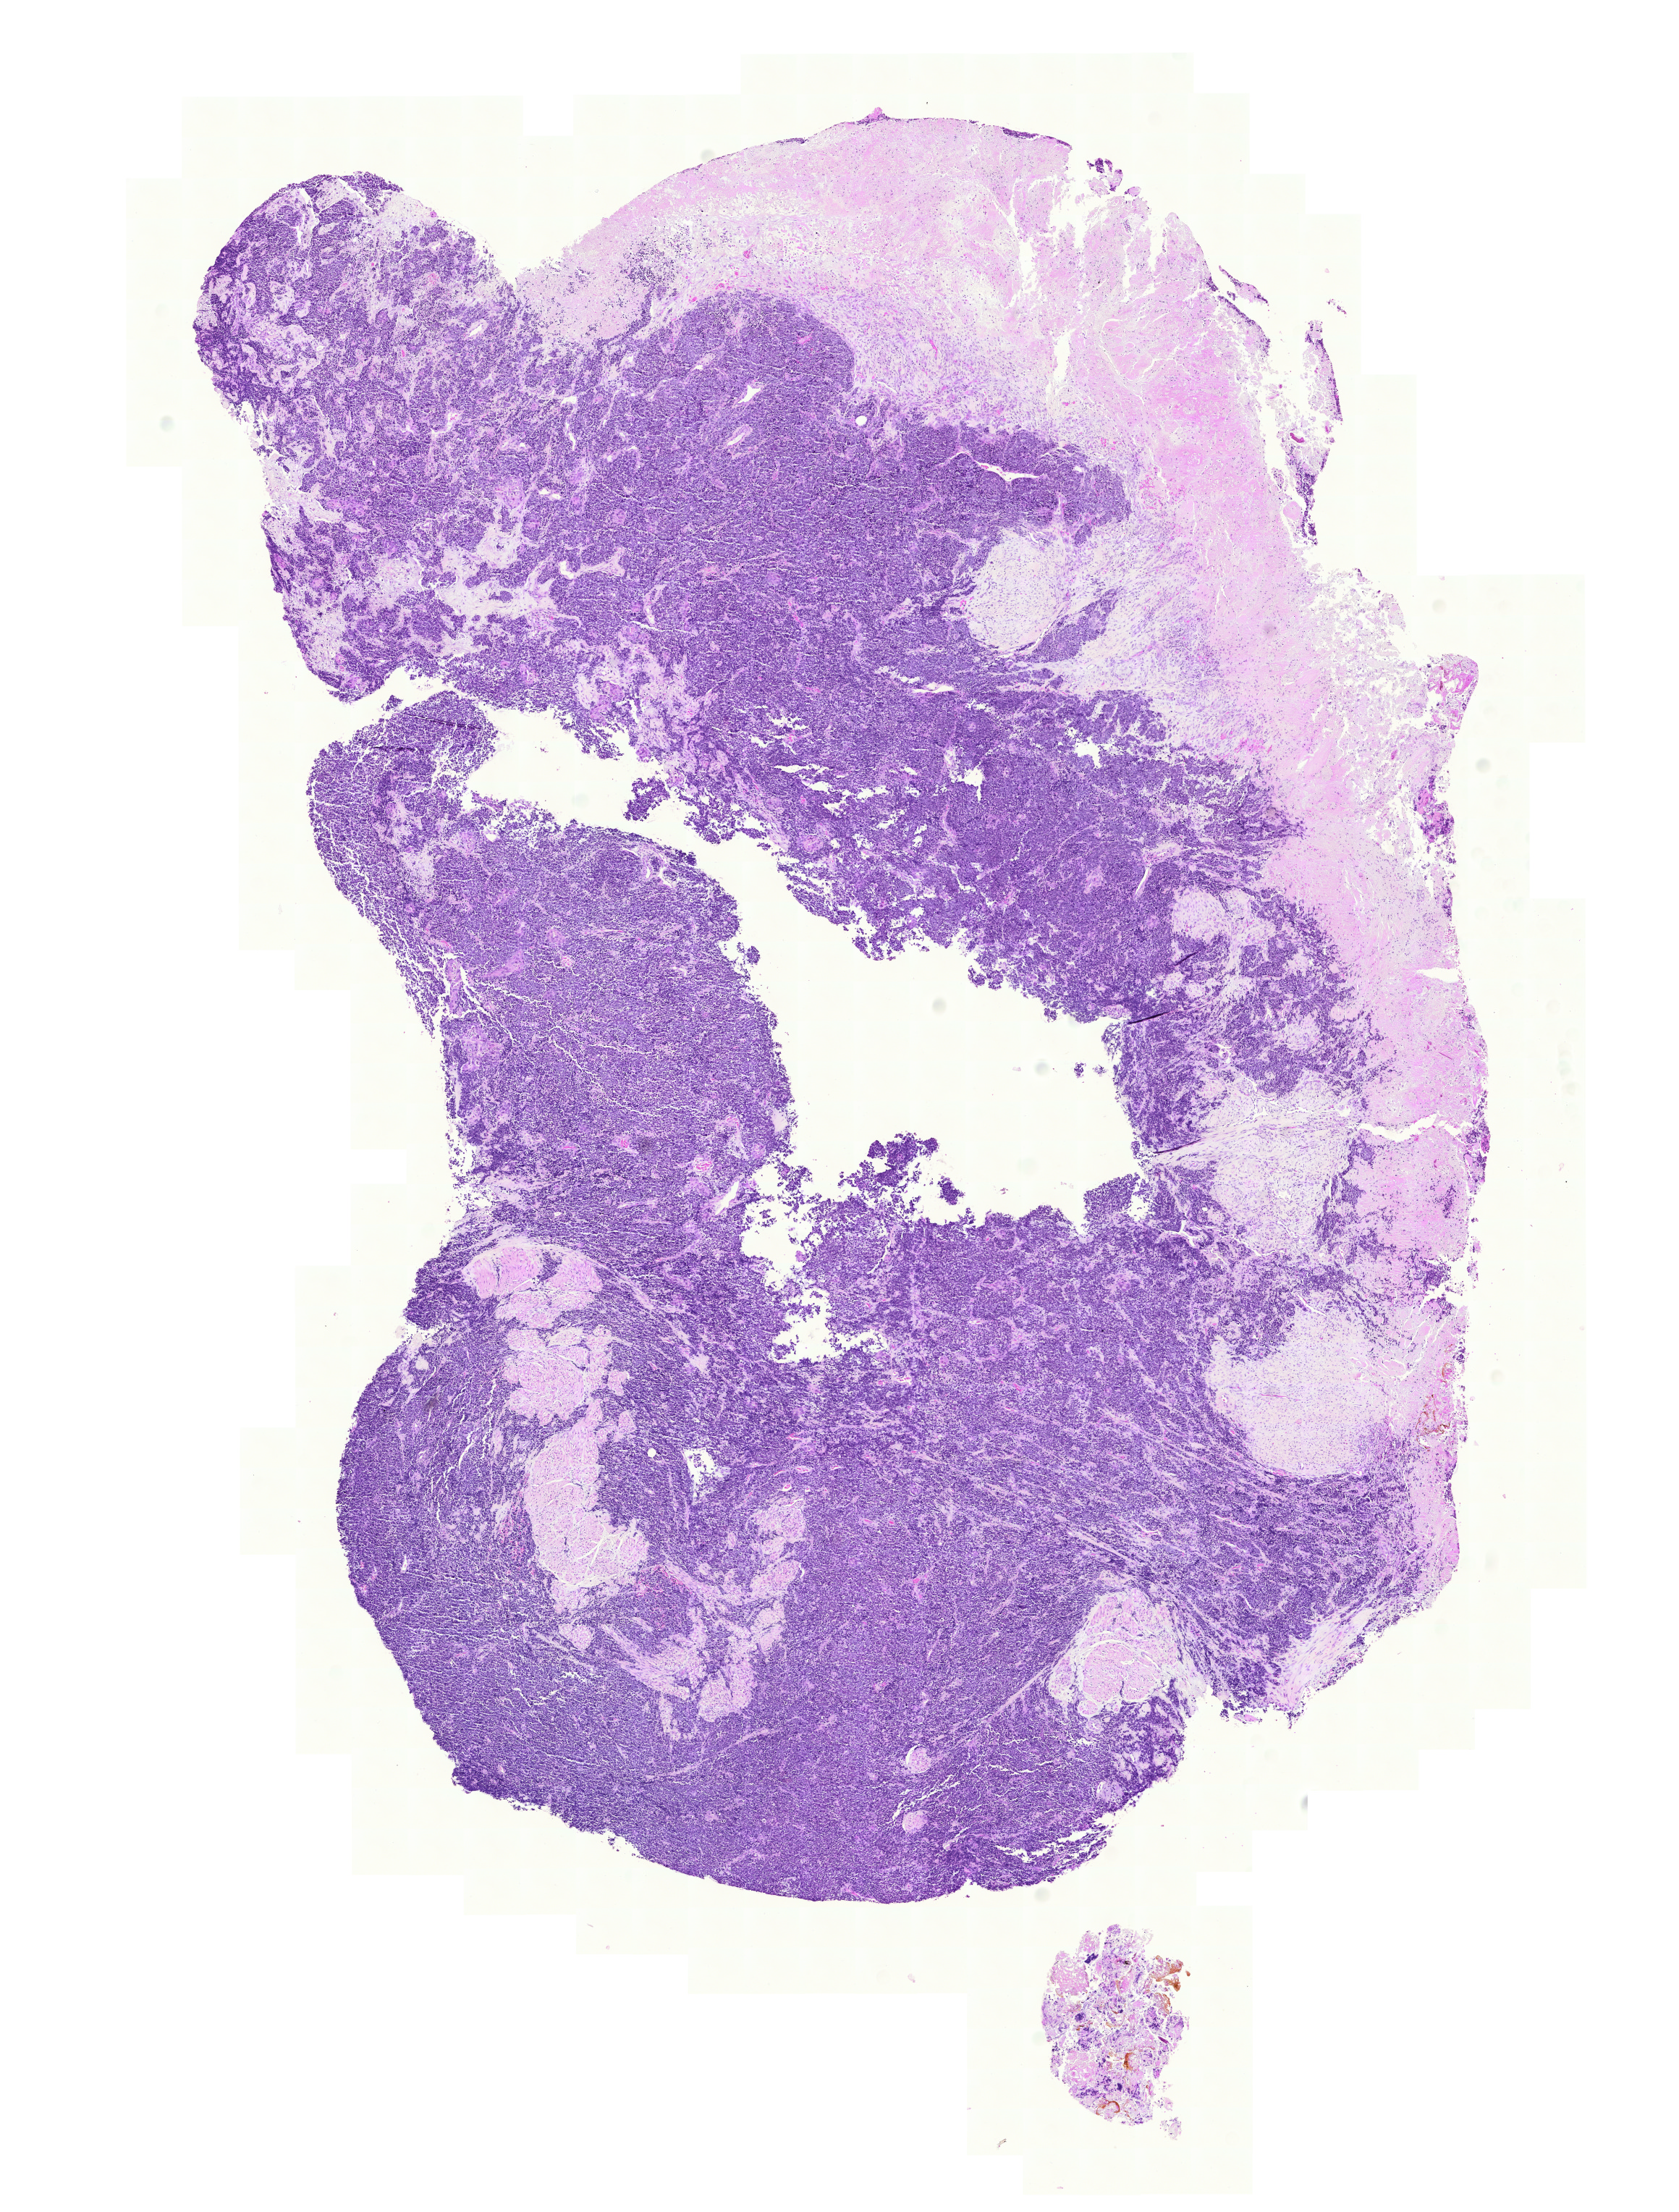
Digitized H&E tissue section (whole slide) — a low-resolution overview of the entire scanned area, about 8.6 x 11.4 mm. Formalin-fixed paraffin-embedded (FFPE) diagnostic section. Bladder, primary tumour sample. Female, age 68 years at initial diagnosis. Histologic grade: high grade.
* AJCC pathologic stage: IV (5th edition)
* diagnosis: Transitional cell carcinoma